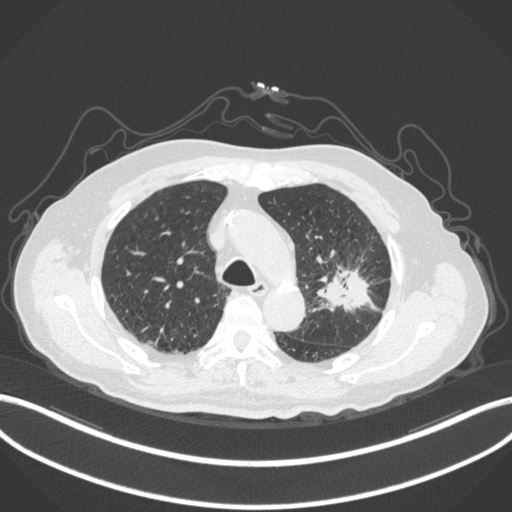
Chest CT, one axial slice. Slice 210 of 331 in the series (ordered by position). 120 kVp. Lung window (W 1500 / L -600 HU). 512 × 512 image matrix, field of view 400 × 400 mm. Patient: male, 79 years. Case-level facts recorded for this patient, not image findings: clinical TNM (as recorded): T2a N1 M1.
Annotated regions visible in this slice (rectangle marked by the reading radiologist):
- lung tumour (recorded histology: adenocarcinoma): bounding box (x1, y1, x2, y2) in pixels: (319, 268, 376, 313)